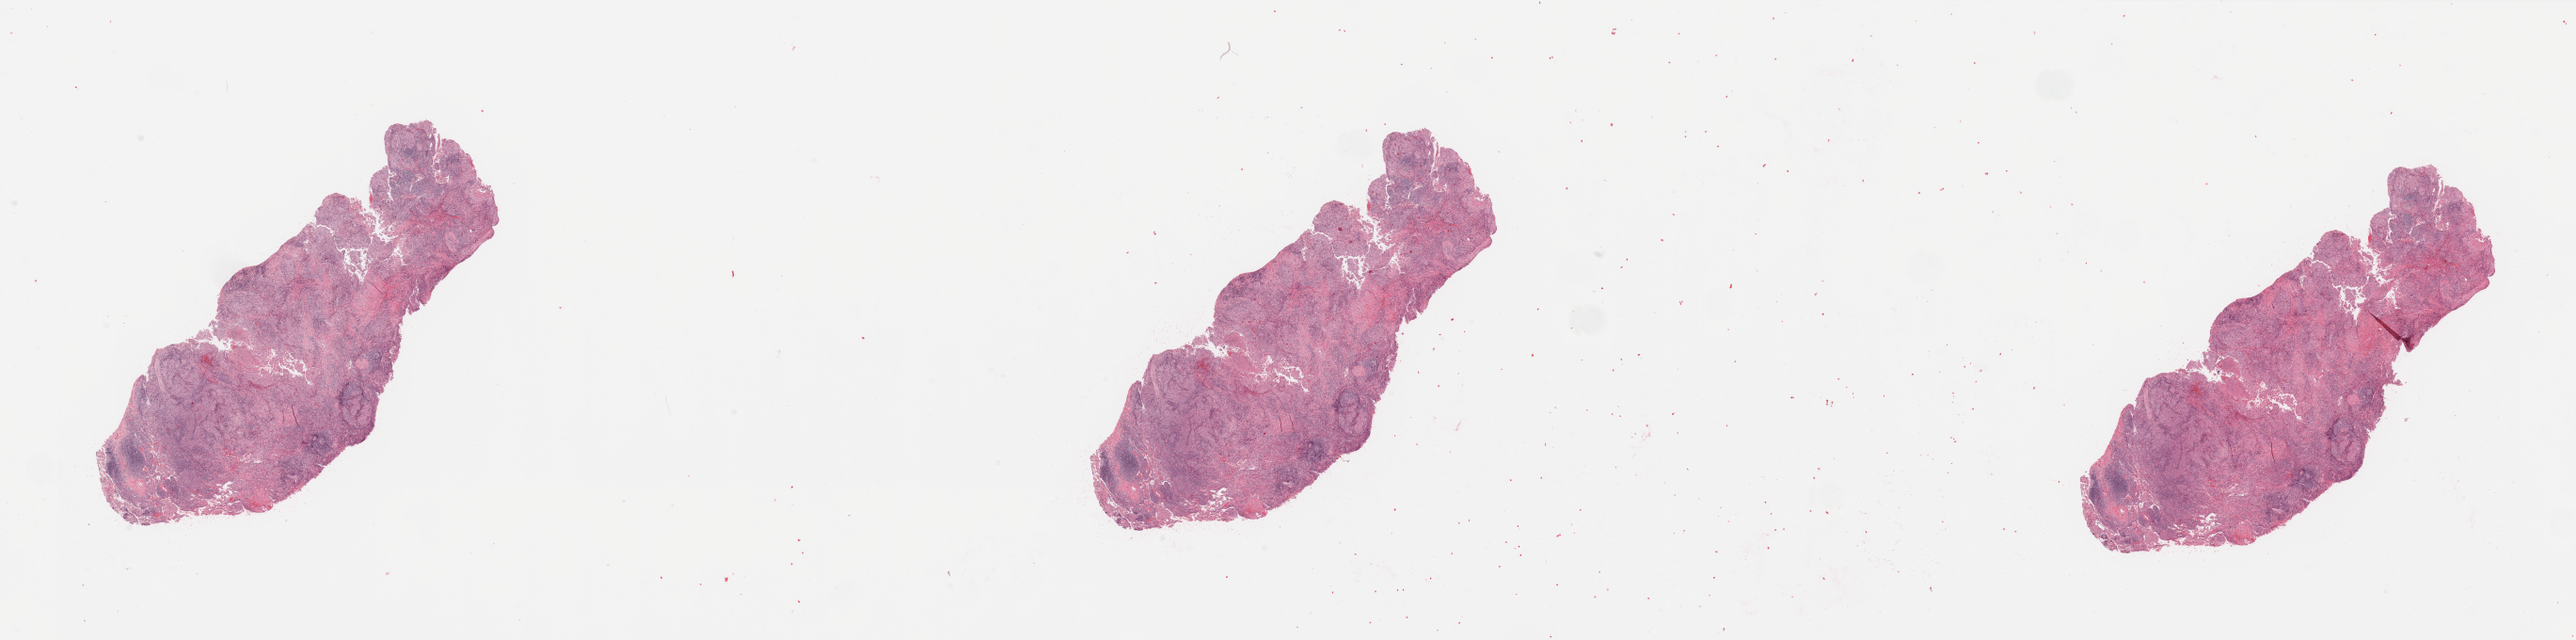
Whole-slide histology image, H&E — a low-resolution overview of the entire scanned area, about 43.3 x 10.8 mm; lung, tumour tissue. 77-year-old female patient. Histologic grade: G3 (poorly differentiated).
* AJCC pathologic stage: IIA
* primary tumour site (as recorded): right lower lobe
* histologic diagnosis: Squamous cell carcinoma, NOS